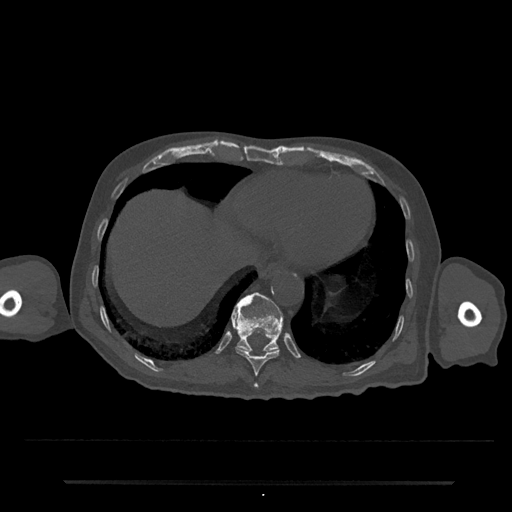
CT including the spine, one axial slice. Position 290 of 797 along the scan axis. 120 kVp. Bone window (W 1800 / L 400 HU). 512 × 512 image matrix. Patient: male, 74 years. Case-level facts recorded for this patient, not image findings: primary cancer: prostate.
Outlined on this slice (semi-automatically segmented with operator editing):
- T10 vertebra: bounding box [x1, y1, x2, y2] px = [235, 336, 279, 376]
- T11 vertebra: [231, 292, 283, 353]
- T9 vertebra: [254, 383, 258, 388]